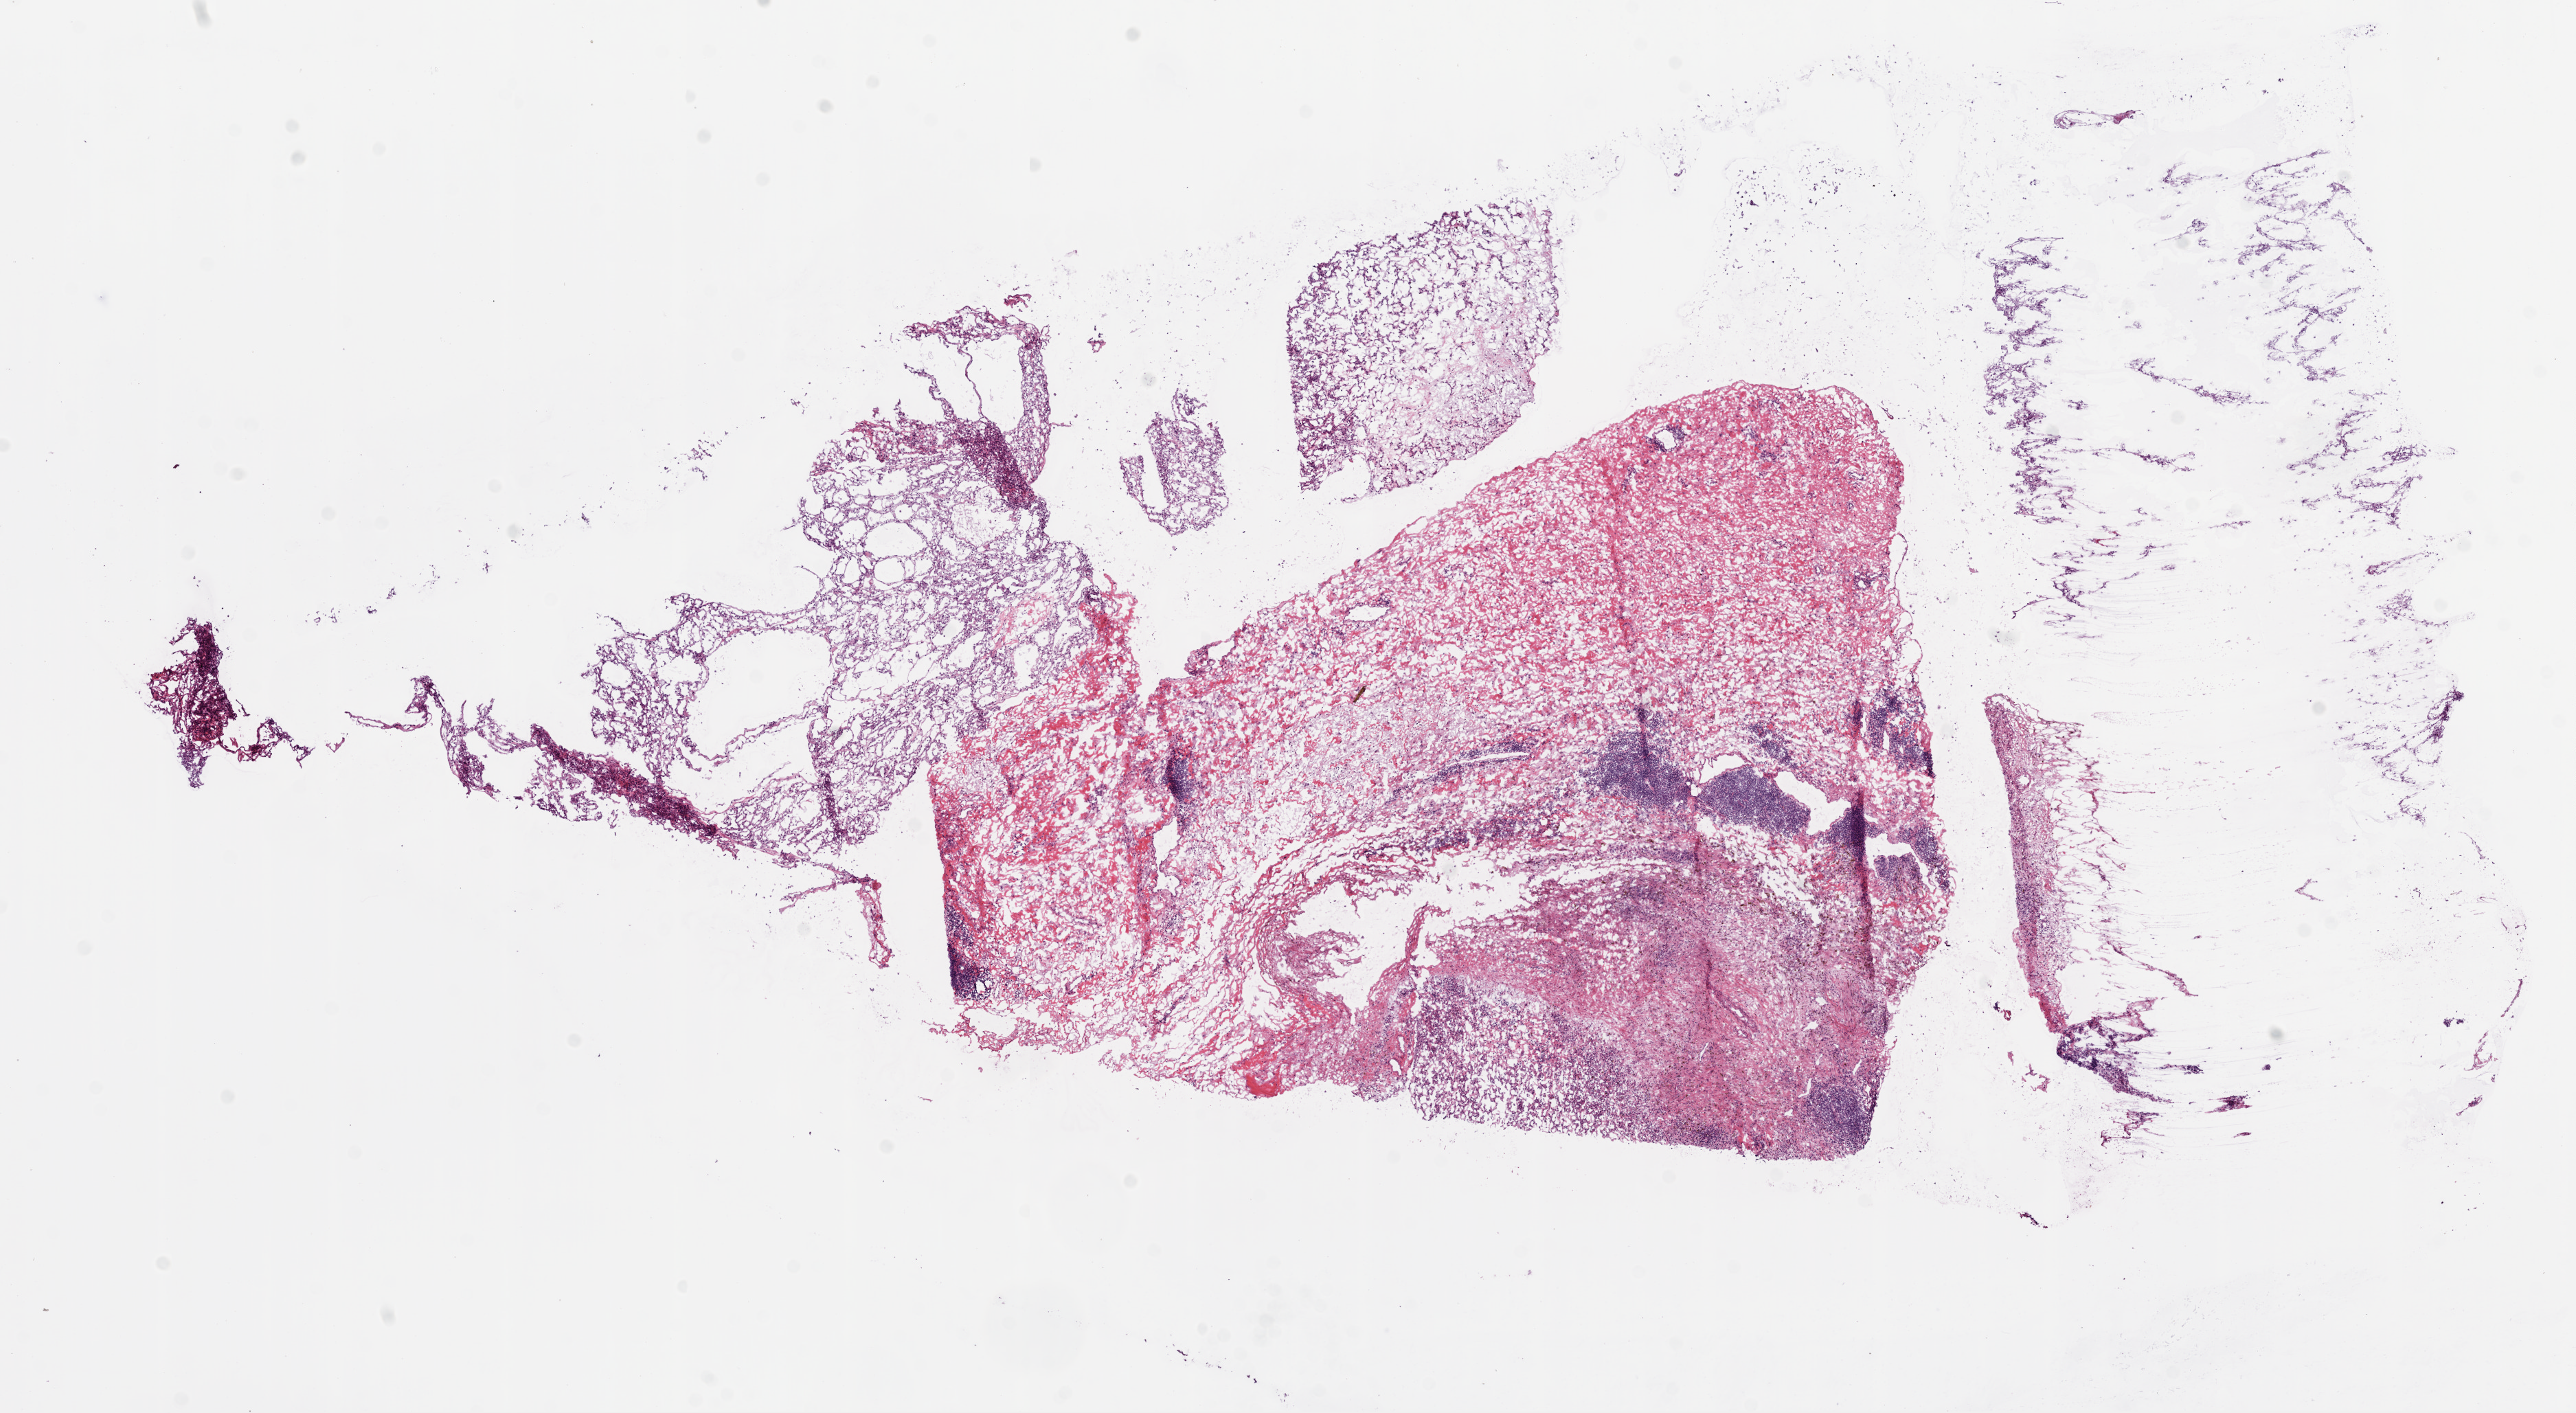
Whole-slide histology image, Hematoxylin and eosin (H&E) stained, shown as a low-resolution overview of the whole scanned area (about 15.0 x 8.3 mm); frozen section; kidney, primary tumour sample. Female patient; age at initial diagnosis 63 years. Histologic grade: G4 (undifferentiated). Composition of this section per pathologist review: tumour cells 35%, tumour nuclei 60%, normal cells 0%, stromal cells 65%, necrosis 0%.
TNM: T1a NX M0. AJCC pathologic stage: I. Lymph nodes positive (case pathology): 0 of 1 examined. Diagnosis: Clear cell adenocarcinoma, NOS.